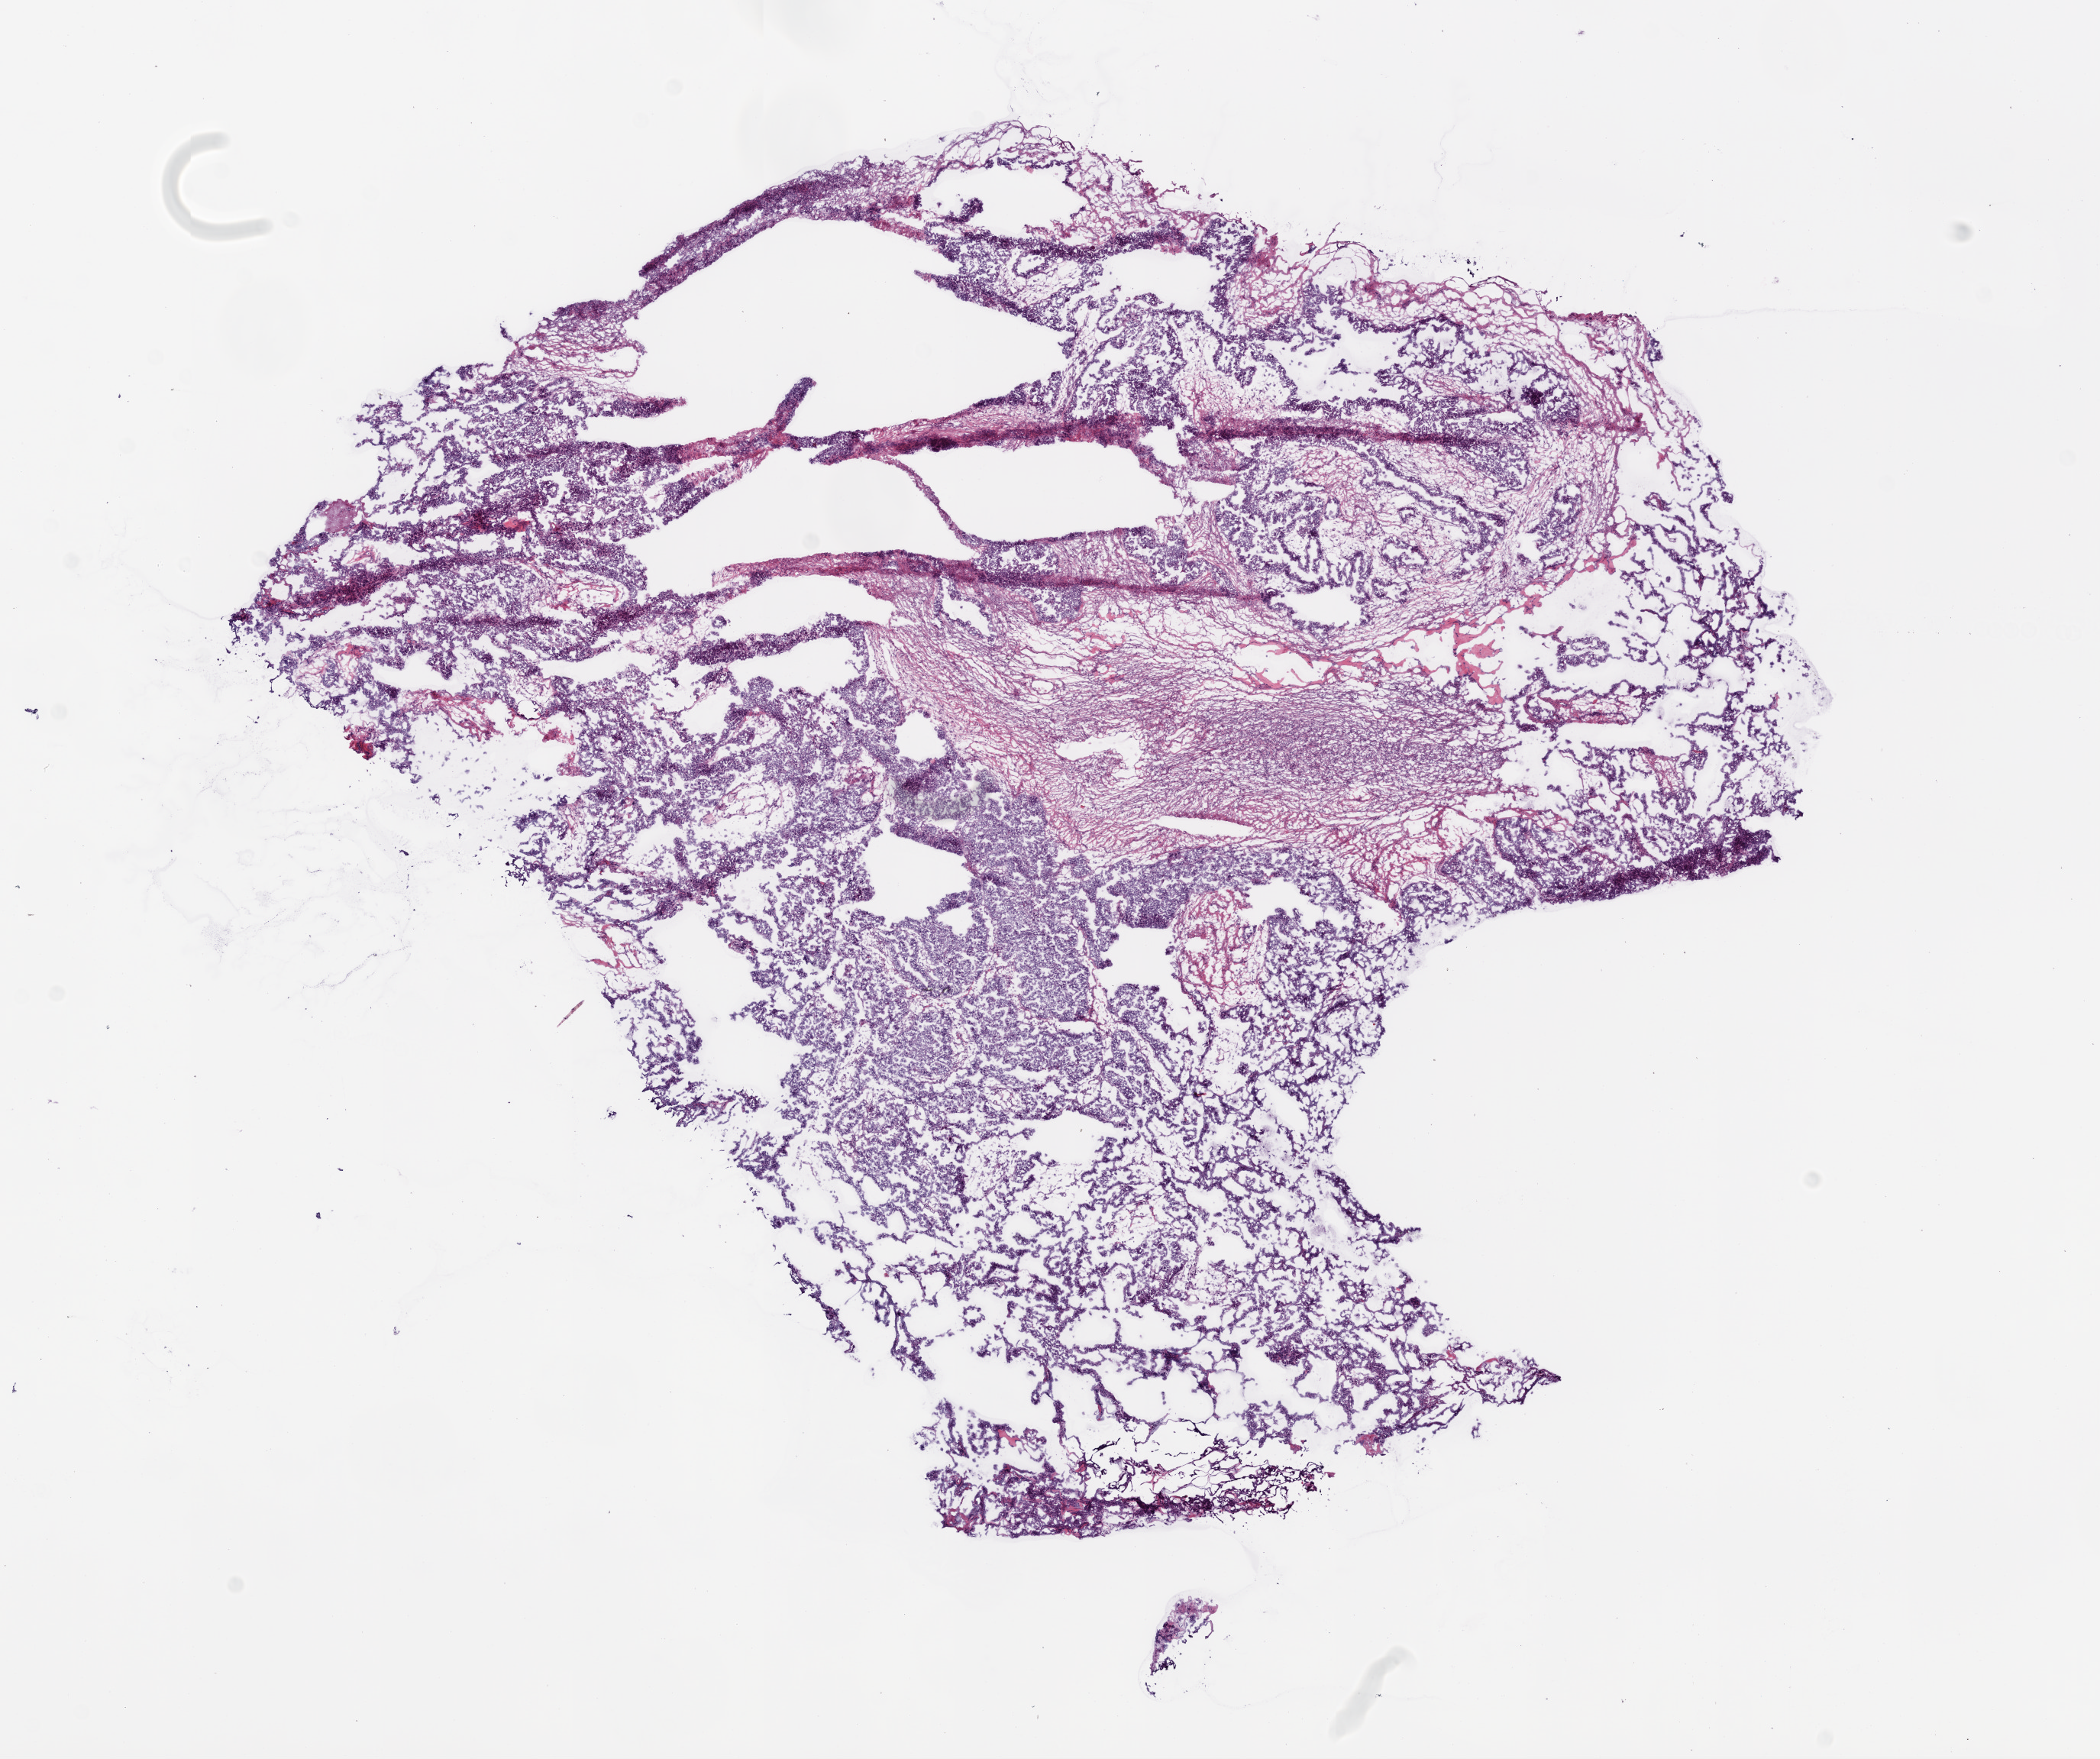
Hematoxylin and eosin (H&E) stained whole-slide image — a low-resolution overview of the entire scanned area, about 11.0 x 9.2 mm; frozen section from the bottom of the tissue portion; sample: primary tumour, ovary. Female patient; age at initial diagnosis 55 years. Histologic grade: G3 (poorly differentiated). Slide review estimates, as recorded: tumour cells 80%, tumour nuclei 80%, normal cells 0%, stromal cells 20%, necrosis 0%.
* pathologic diagnosis: Serous cystadenocarcinoma, NOS
* FIGO stage: IIIC